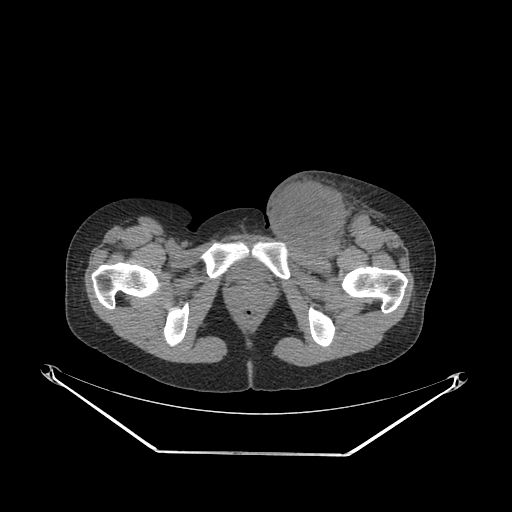
CT of an extremity soft-tissue mass (from a PET/CT study), one axial slice; position 63 of 267 along the scan axis; reconstruction kernel SOFT; 140 kVp; soft-tissue window (W 400 / L 40 HU); 3.75 mm slice thickness; 512 × 512 image matrix, field of view 500 × 500 mm. Female patient. From the clinical record (not read from this slice): histological type: leiomyosarcoma; grade: high; site of the primary tumour: groin.
Outlined on this slice (expert contour drawn on MRI and transferred to this co-registered scan by the dataset authors):
- gross tumour volume including surrounding oedema: bounding box <262,173,382,254> (left, top, right, bottom; pixels)
- gross tumour volume (mass): <263,180,348,254>